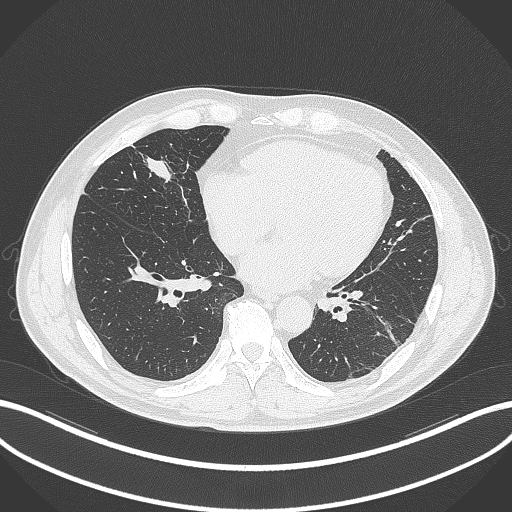
Chest CT, one axial slice. Slice 101 of 399 in the series (ordered by position). 120 kVp. Lung window (W 1500 / L -600 HU). 1 mm slice thickness. 512 × 512 image matrix, field of view 400 × 400 mm. Male patient, age 59 years. Case-level facts recorded for this patient, not image findings: clinical TNM (as recorded): T2a N1 M0.
Structures marked on this image (bounding box drawn by a radiologist):
- lung tumour (recorded histology: adenocarcinoma): box from (x=141, y=150) to (x=181, y=189) px